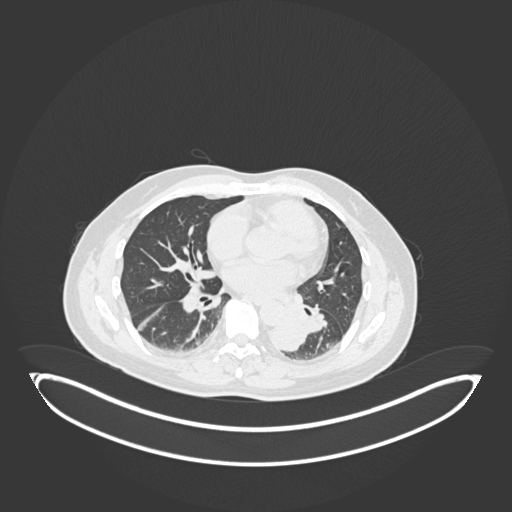
Chest CT, one axial slice; reconstruction kernel B30f; lung window (W 1500 / L -600 HU); 512 × 512 image matrix, field of view 500 × 500 mm. Patient: male, 54 years. From the clinical record (not read from this slice): clinical TNM (as recorded): T3 N0 M0.
Annotated regions visible in this slice (bounding box drawn by a radiologist):
- lung tumour (recorded histology: squamous cell carcinoma): bounding box <262,303,307,353> (left, top, right, bottom; pixels)